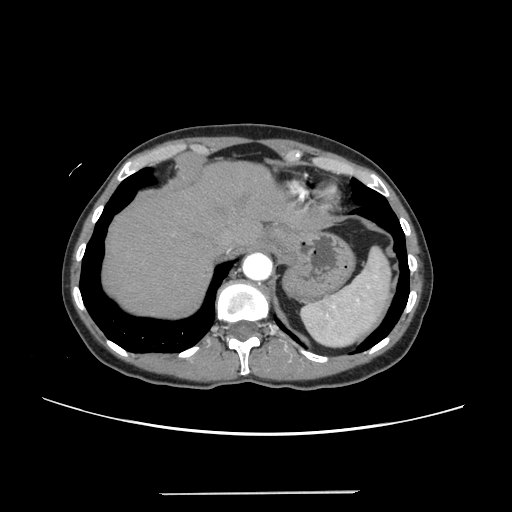
Contrast-enhanced abdominal CT, one axial slice. Slice 205 of 240 in the series (ordered by position). Intravenous contrast given. Soft-tissue window (W 400 / L 40 HU). 1.25 mm slice thickness. 512 × 512 image matrix, field of view 371 × 371 mm. Female patient, age 60 years. From the clinical record (not read from this slice): diagnosis: colorectal cancer liver metastases, imaged before liver resection; multiple liver metastases: no; largest metastasis: 1.5 cm; disease in both lobes: no.
Structures marked on this image (outlined manually by an expert reader):
- hepatic veins: box from (x=221, y=224) to (x=250, y=250) px
- liver: (x=103, y=162)–(x=310, y=316)
- planned liver remnant (the part of the liver to remain after resection): (x=103, y=162)–(x=305, y=316)